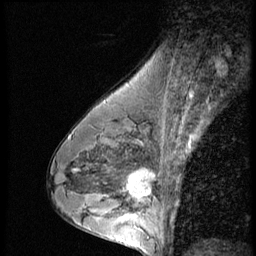
Breast MRI (dynamic contrast-enhanced), one sagittal slice. Slice 35 of 56 in the series (ordered by position). 3 images stored at this slice position (order not interpretable as contrast timing). 1.5 T. TE 4.2 ms, TR 9 ms. 256 × 256 image matrix. Patient: female, 43 years. From the clinical record (not read from this slice): setting: breast cancer imaged before/during neoadjuvant chemotherapy; receptor status: HR-positive, HER2-negative.
Annotated regions visible in this slice (semi-automatic segmentation, software-assisted and operator-edited):
- analysis volume of interest (the breast-tissue region the enhancement analysis was run in; not a lesion): bounding box [x1, y1, x2, y2] px = [120, 160, 163, 207]
- tumour enhancement mask (voxels above the 140 % enhancement threshold inside the analysis volume of interest): [127, 170, 156, 199]